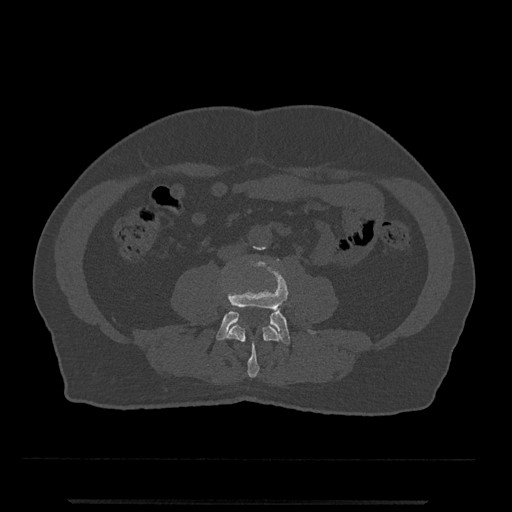
CT including the spine, one axial slice. Slice 165 of 797 in the series (ordered by position). Reconstruction kernel Br40s/3. Bone window (W 1800 / L 400 HU). 0.5 mm slice thickness. 512 × 512 image matrix, field of view 419 × 419 mm. Patient: male, 63 years. From the clinical record (not read from this slice): primary cancer: prostate.
Outlined on this slice (semi-automatic segmentation, software-assisted and operator-edited):
- L3 vertebra: bounding box (x1, y1, x2, y2) in pixels: (226, 324, 280, 378)
- L4 vertebra: (216, 262, 315, 345)